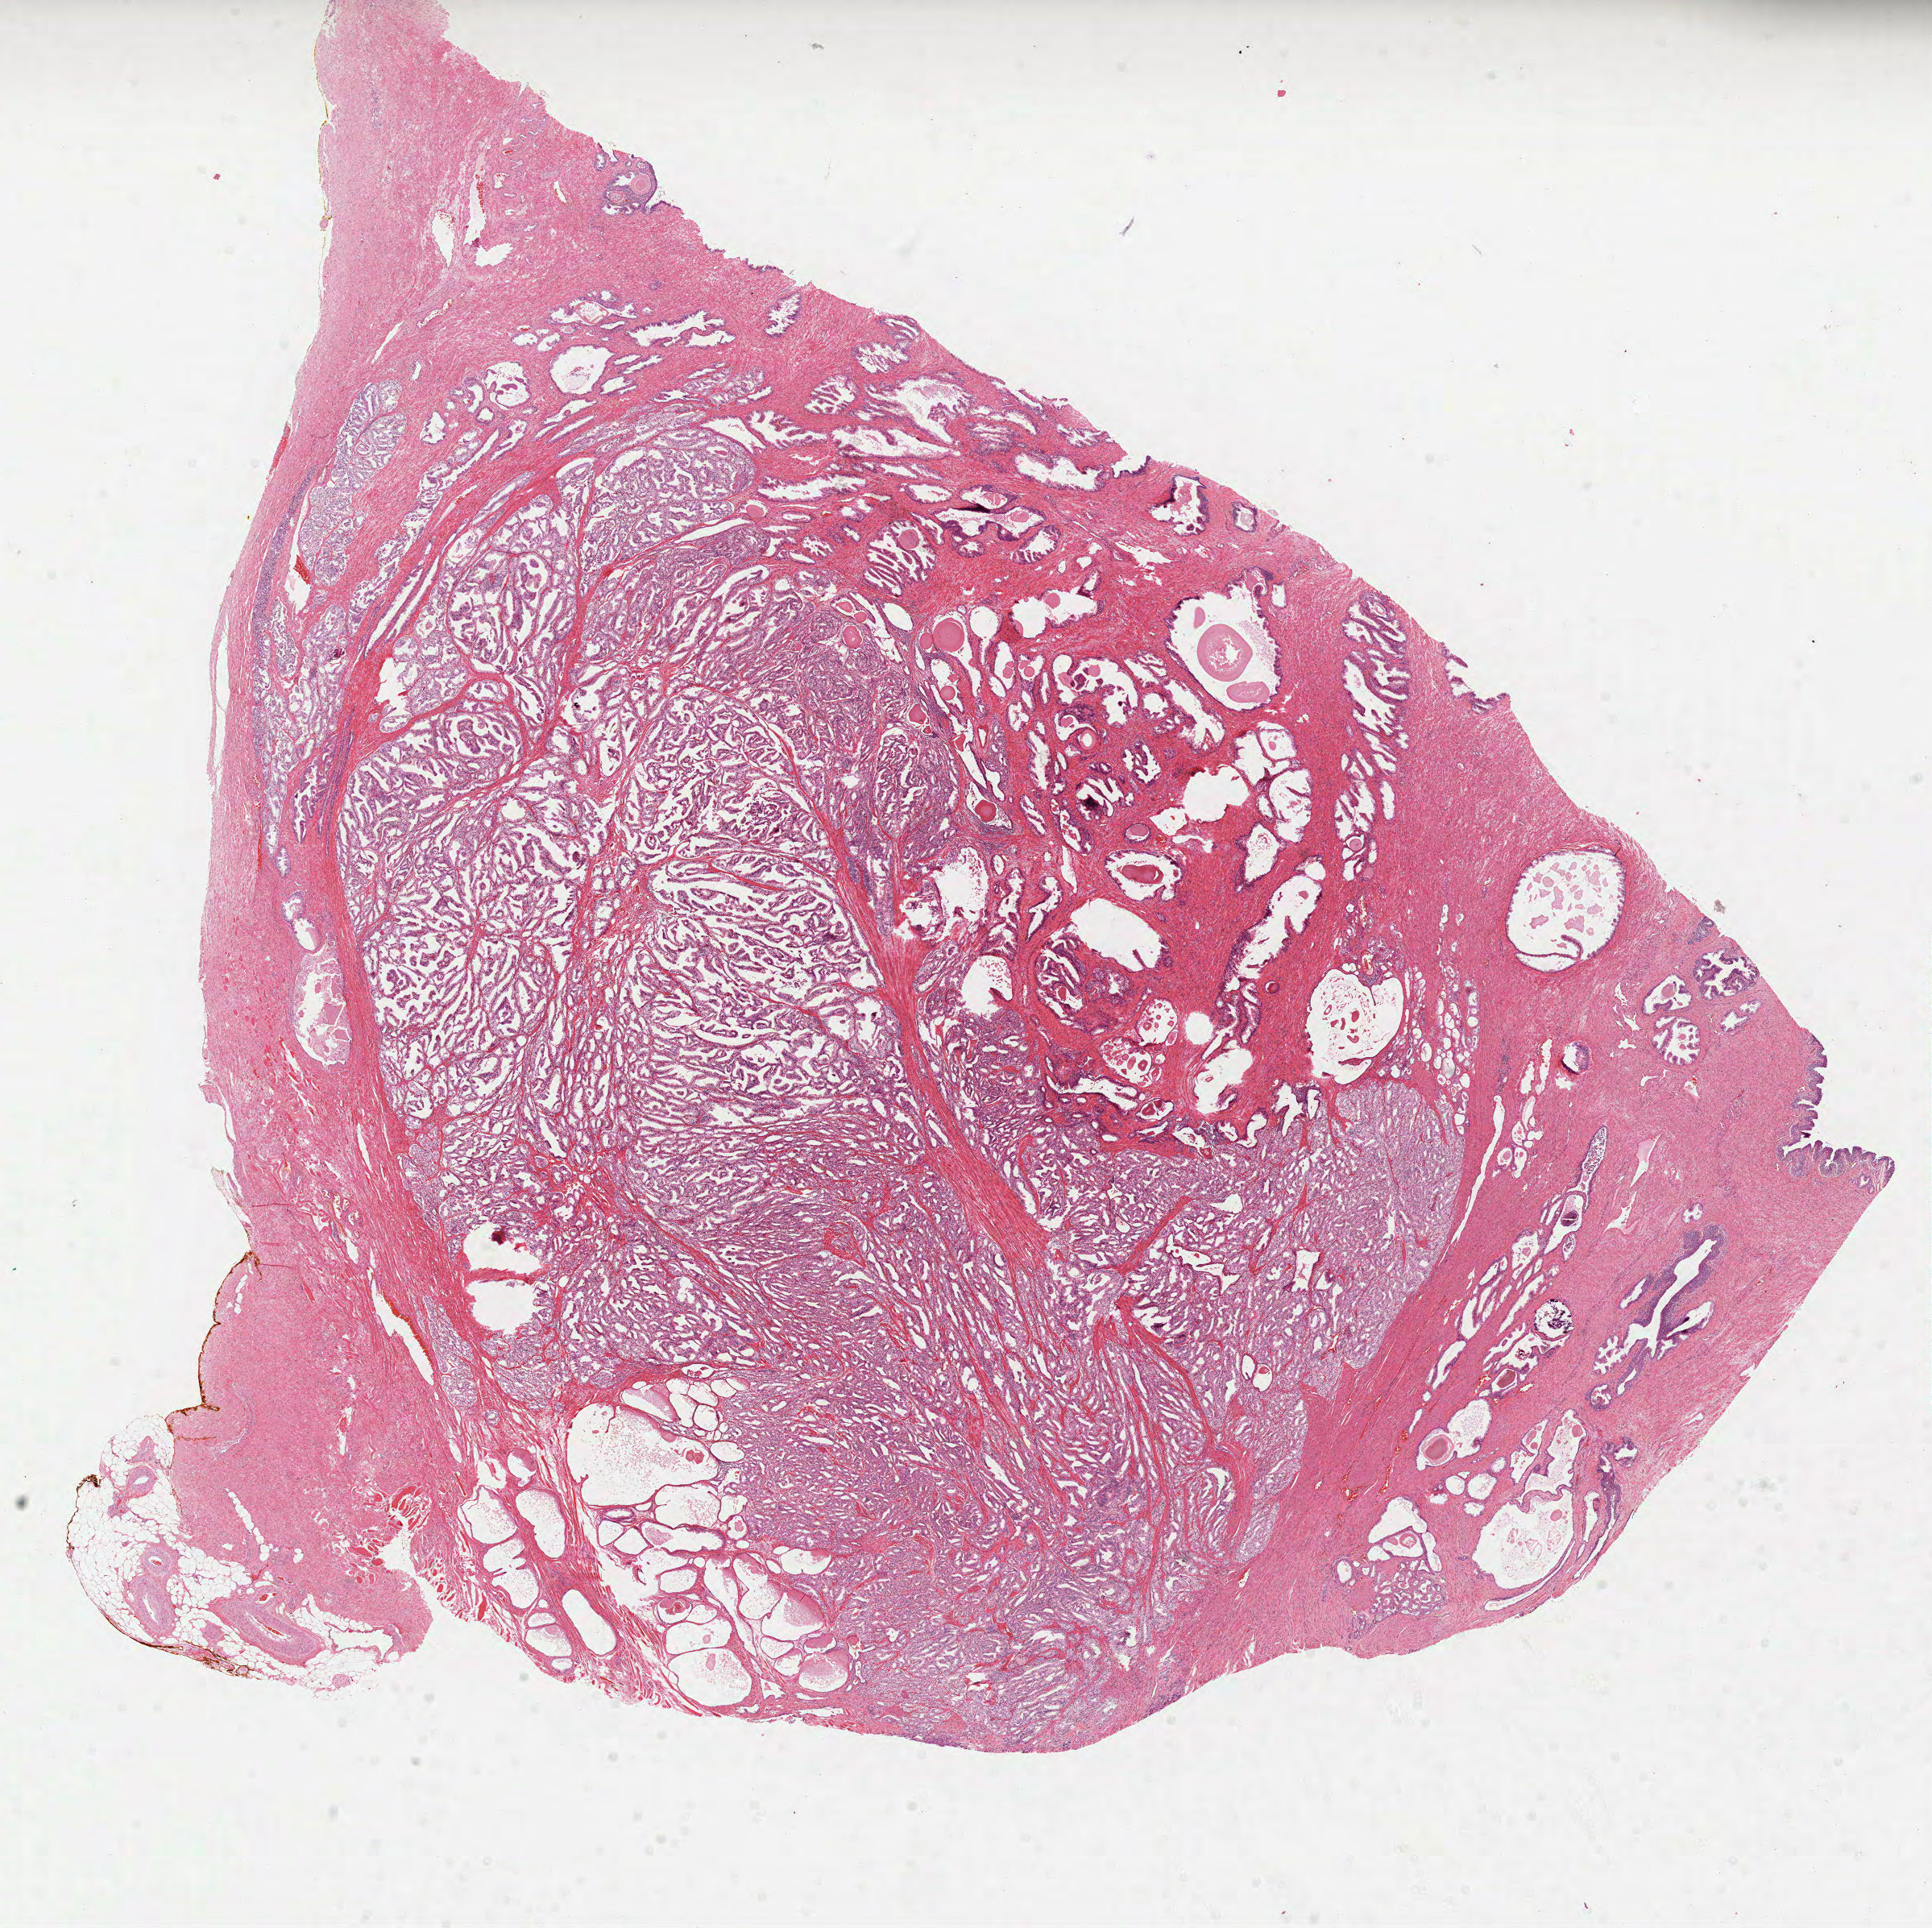
Whole-slide histology image, H&E, a low-resolution overview of the entire scanned area, about 19.3 x 19.3 mm (from a 40x scan); formalin-fixed paraffin-embedded (FFPE) diagnostic section; primary tumour sample from the prostate. Male, age 61 years at initial diagnosis. Gleason score: 7 (4+3).
* pathologic diagnosis: Acinar cell carcinoma (prostate gland)